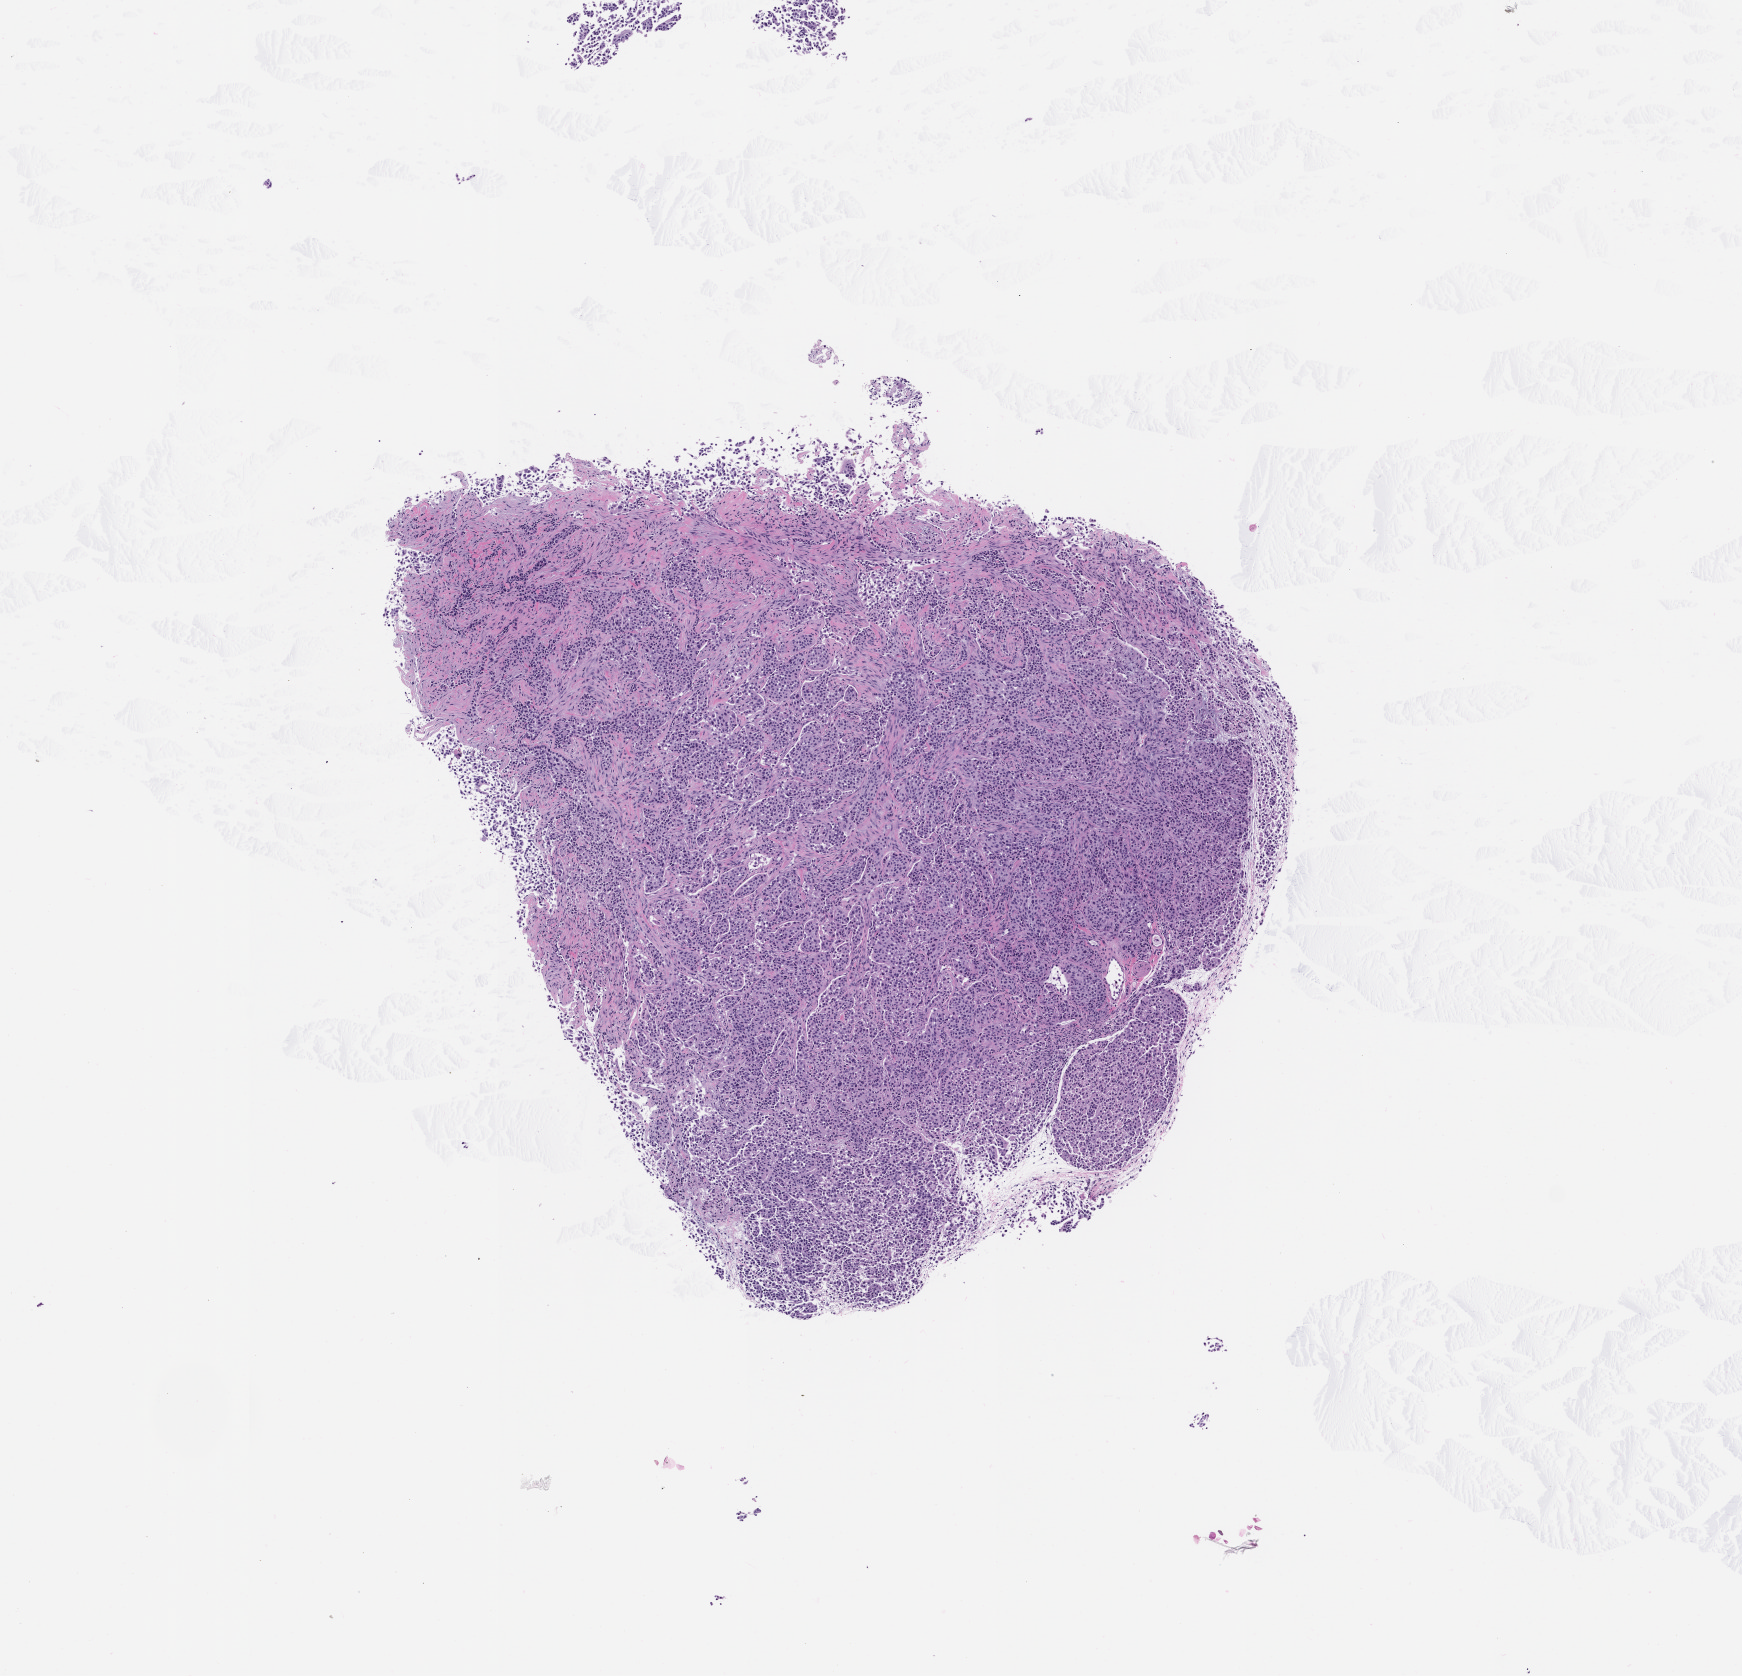
Whole-slide image, hematoxylin and eosin (H&E): patient-derived xenograft (human tumor grown in a mouse), passage 1 — whole scanned area (about 7.0 x 6.7 mm) shown as a low-resolution overview; formalin-fixed, paraffin-embedded (FFPE) tissue; tumor site category: bladder.
- originating patient diagnosis: Transitional Cell Carcinoma